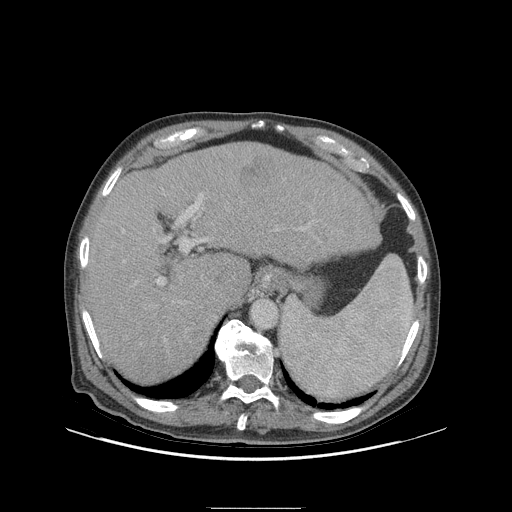
Contrast-enhanced abdominal CT (liver protocol), one axial slice; position 71 of 105 along the scan axis; 140 kVp; soft-tissue window (W 400 / L 40 HU); 2.5 mm slice thickness; 512 × 512 image matrix, field of view 440 × 440 mm. Case-level facts recorded for this patient, not image findings: diagnosis: hepatocellular carcinoma (patient treated with transarterial chemoembolisation; whether this scan precedes or follows treatment is not stated here); TNM stage (as recorded): Stage-I; Child-Pugh class: A; tumour nodularity: uninodular; tumour size: 5.1 cm.
Outlined on this slice (semi-automatic segmentation, software-assisted and operator-edited):
- liver parenchyma outside the tumour (the mass and vessels are separate outlines, so this box may not span the whole liver): bounding box <86,142,380,384> (left, top, right, bottom; pixels)
- mass: <238,155,273,188>
- liver vessels: <100,193,306,355>